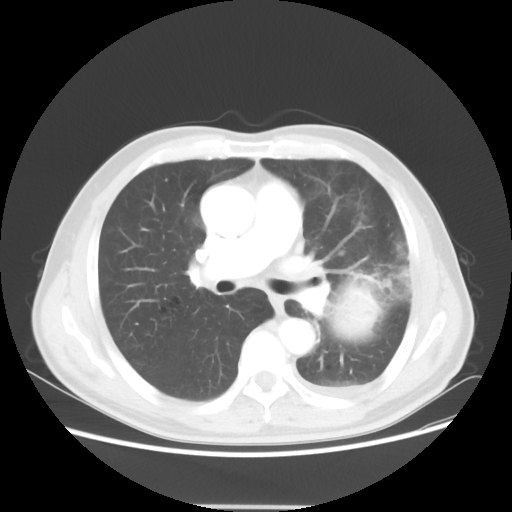
Chest CT, one axial slice. Slice 31 of 53 in the series (ordered by position). 100 kVp. Lung window (W 1500 / L -600 HU). 5 mm slice thickness. 512 × 512 image matrix, field of view 391 × 391 mm. Male patient, age 60 years. From the clinical record (not read from this slice): clinical TNM (as recorded): T4 N1 M1a; histopathological grade: G3.
Outlined on this slice (bounding box drawn by a radiologist):
- lung tumour (recorded histology: large cell carcinoma): bounding box <331,280,387,345> (left, top, right, bottom; pixels)